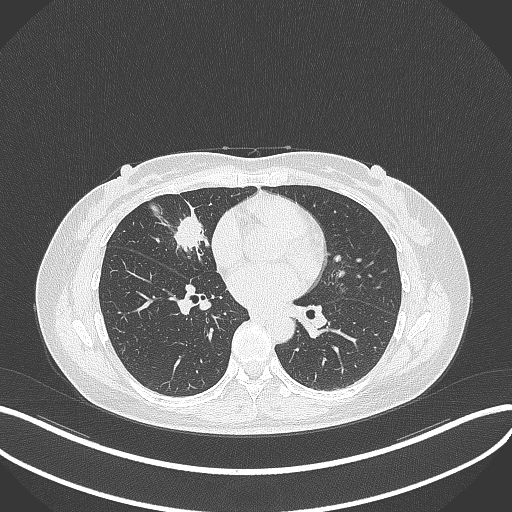
Chest CT, one axial slice; slice 136 of 284 in the series (ordered by position); reconstruction kernel B70f; 120 kVp; lung window (W 1500 / L -600 HU); 1 mm slice thickness; 512 × 512 image matrix, field of view 400 × 400 mm. Female patient, age 43 years. From the clinical record (not read from this slice): clinical TNM (as recorded): T1c N3 M1; histopathological grade: G1.
Structures marked on this image (rectangle marked by the reading radiologist):
- lung tumour (recorded histology: adenocarcinoma): bounding box (x1, y1, x2, y2) in pixels: (175, 212, 207, 259)